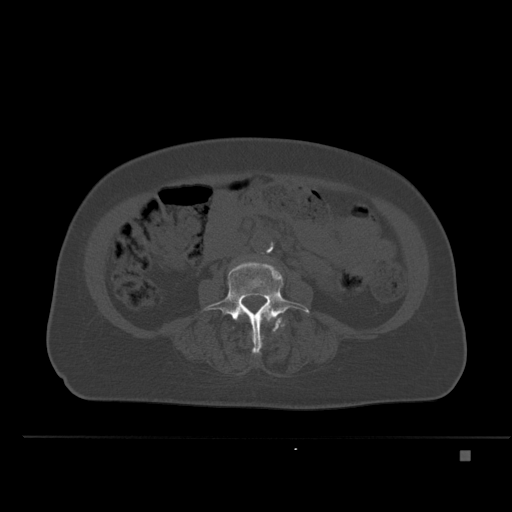
CT including the spine, one axial slice. Slice 182 of 477 in the series (ordered by position). Bone window (W 1800 / L 400 HU). 512 × 512 image matrix. Patient: female, 74 years. Case-level facts recorded for this patient, not image findings: primary cancer: colon.
Structures marked on this image (semi-automatic segmentation, software-assisted and operator-edited):
- L3 vertebra: bounding box <255,311,271,353> (left, top, right, bottom; pixels)
- L4 vertebra: <202,262,309,354>
- L5 vertebra: <279,323,283,326>